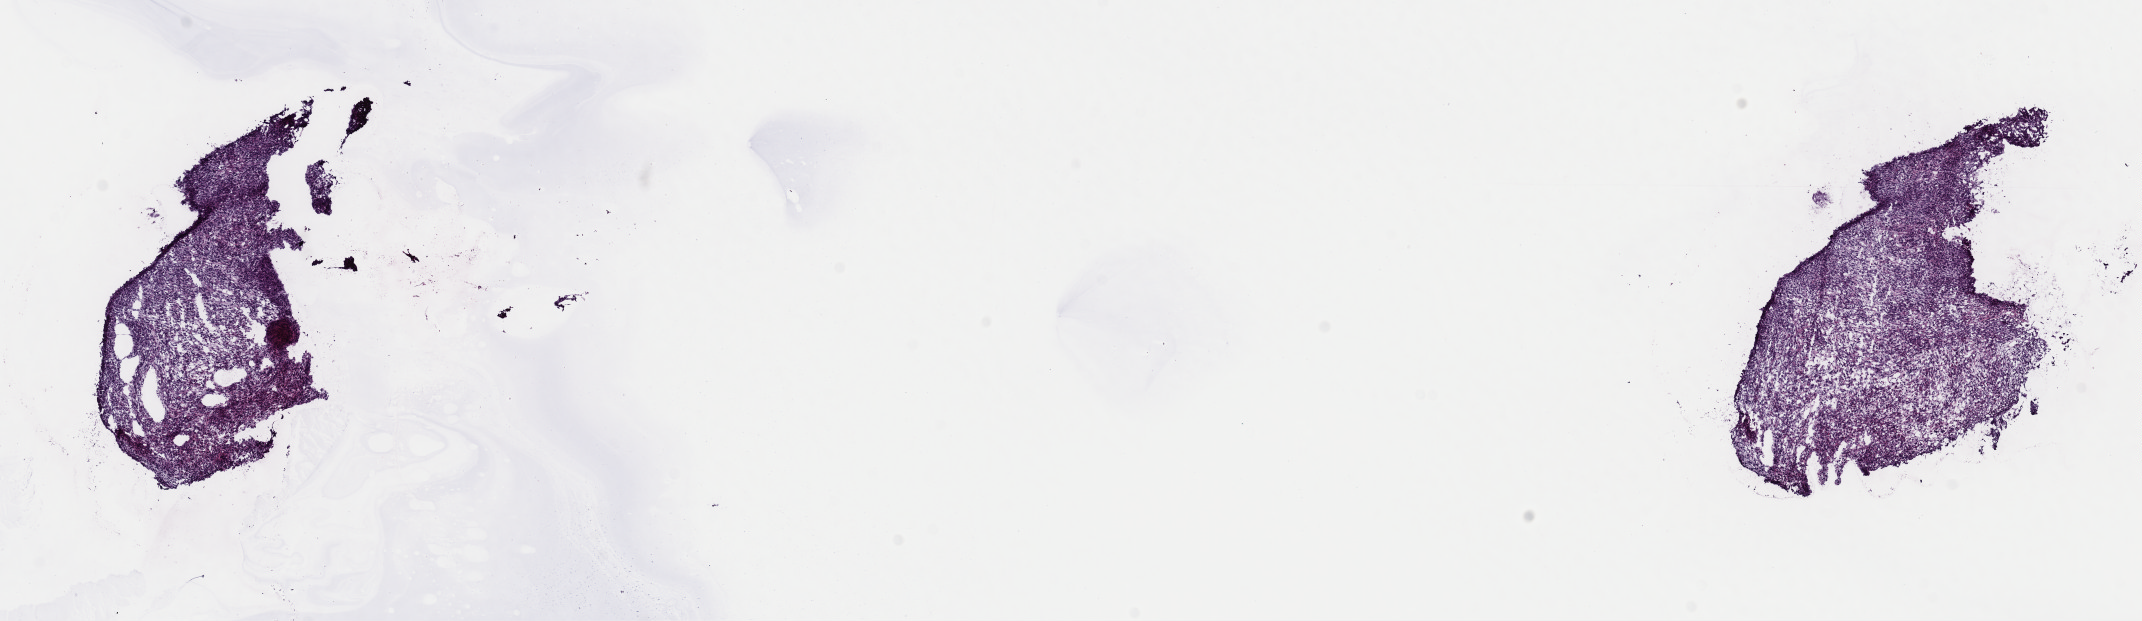
Hematoxylin and eosin (H&E) stained whole-slide image, shown as a low-resolution overview of the whole scanned area (about 16.9 x 4.9 mm); frozen section; sample: primary tumour, uterus. Female, age 68 years at initial diagnosis. Slide review estimates, as recorded: tumour cells 85%, tumour nuclei 85%, normal cells 0%, stromal cells 5%, necrosis 10%. Infiltration values recorded for this section: lymphocyte infiltration 40%, monocyte infiltration 20%, neutrophil infiltration 20%.
Histologic diagnosis: Carcinosarcoma, NOS (endometrium). FIGO stage: IIIC1.